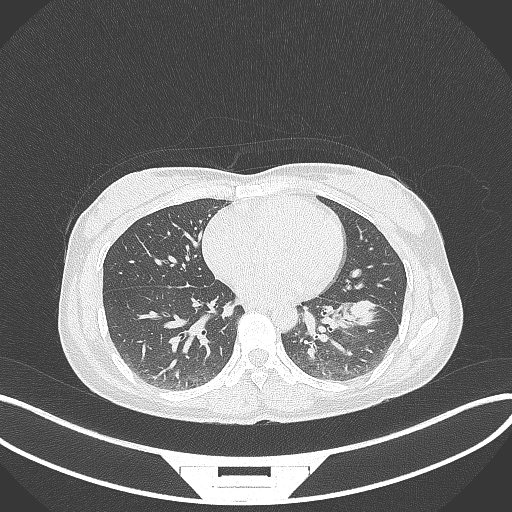
Chest CT, one axial slice; position 33 of 244 along the scan axis; 120 kVp; lung window (W 1500 / L -600 HU); 1 mm slice thickness; 512 × 512 image matrix, field of view 400 × 400 mm. Female patient, age 41 years. From the clinical record (not read from this slice): clinical TNM (as recorded): T2a N3 M1b.
Outlined on this slice (bounding box drawn by a radiologist):
- lung tumour (recorded histology: adenocarcinoma): box from (x=344, y=300) to (x=384, y=329) px